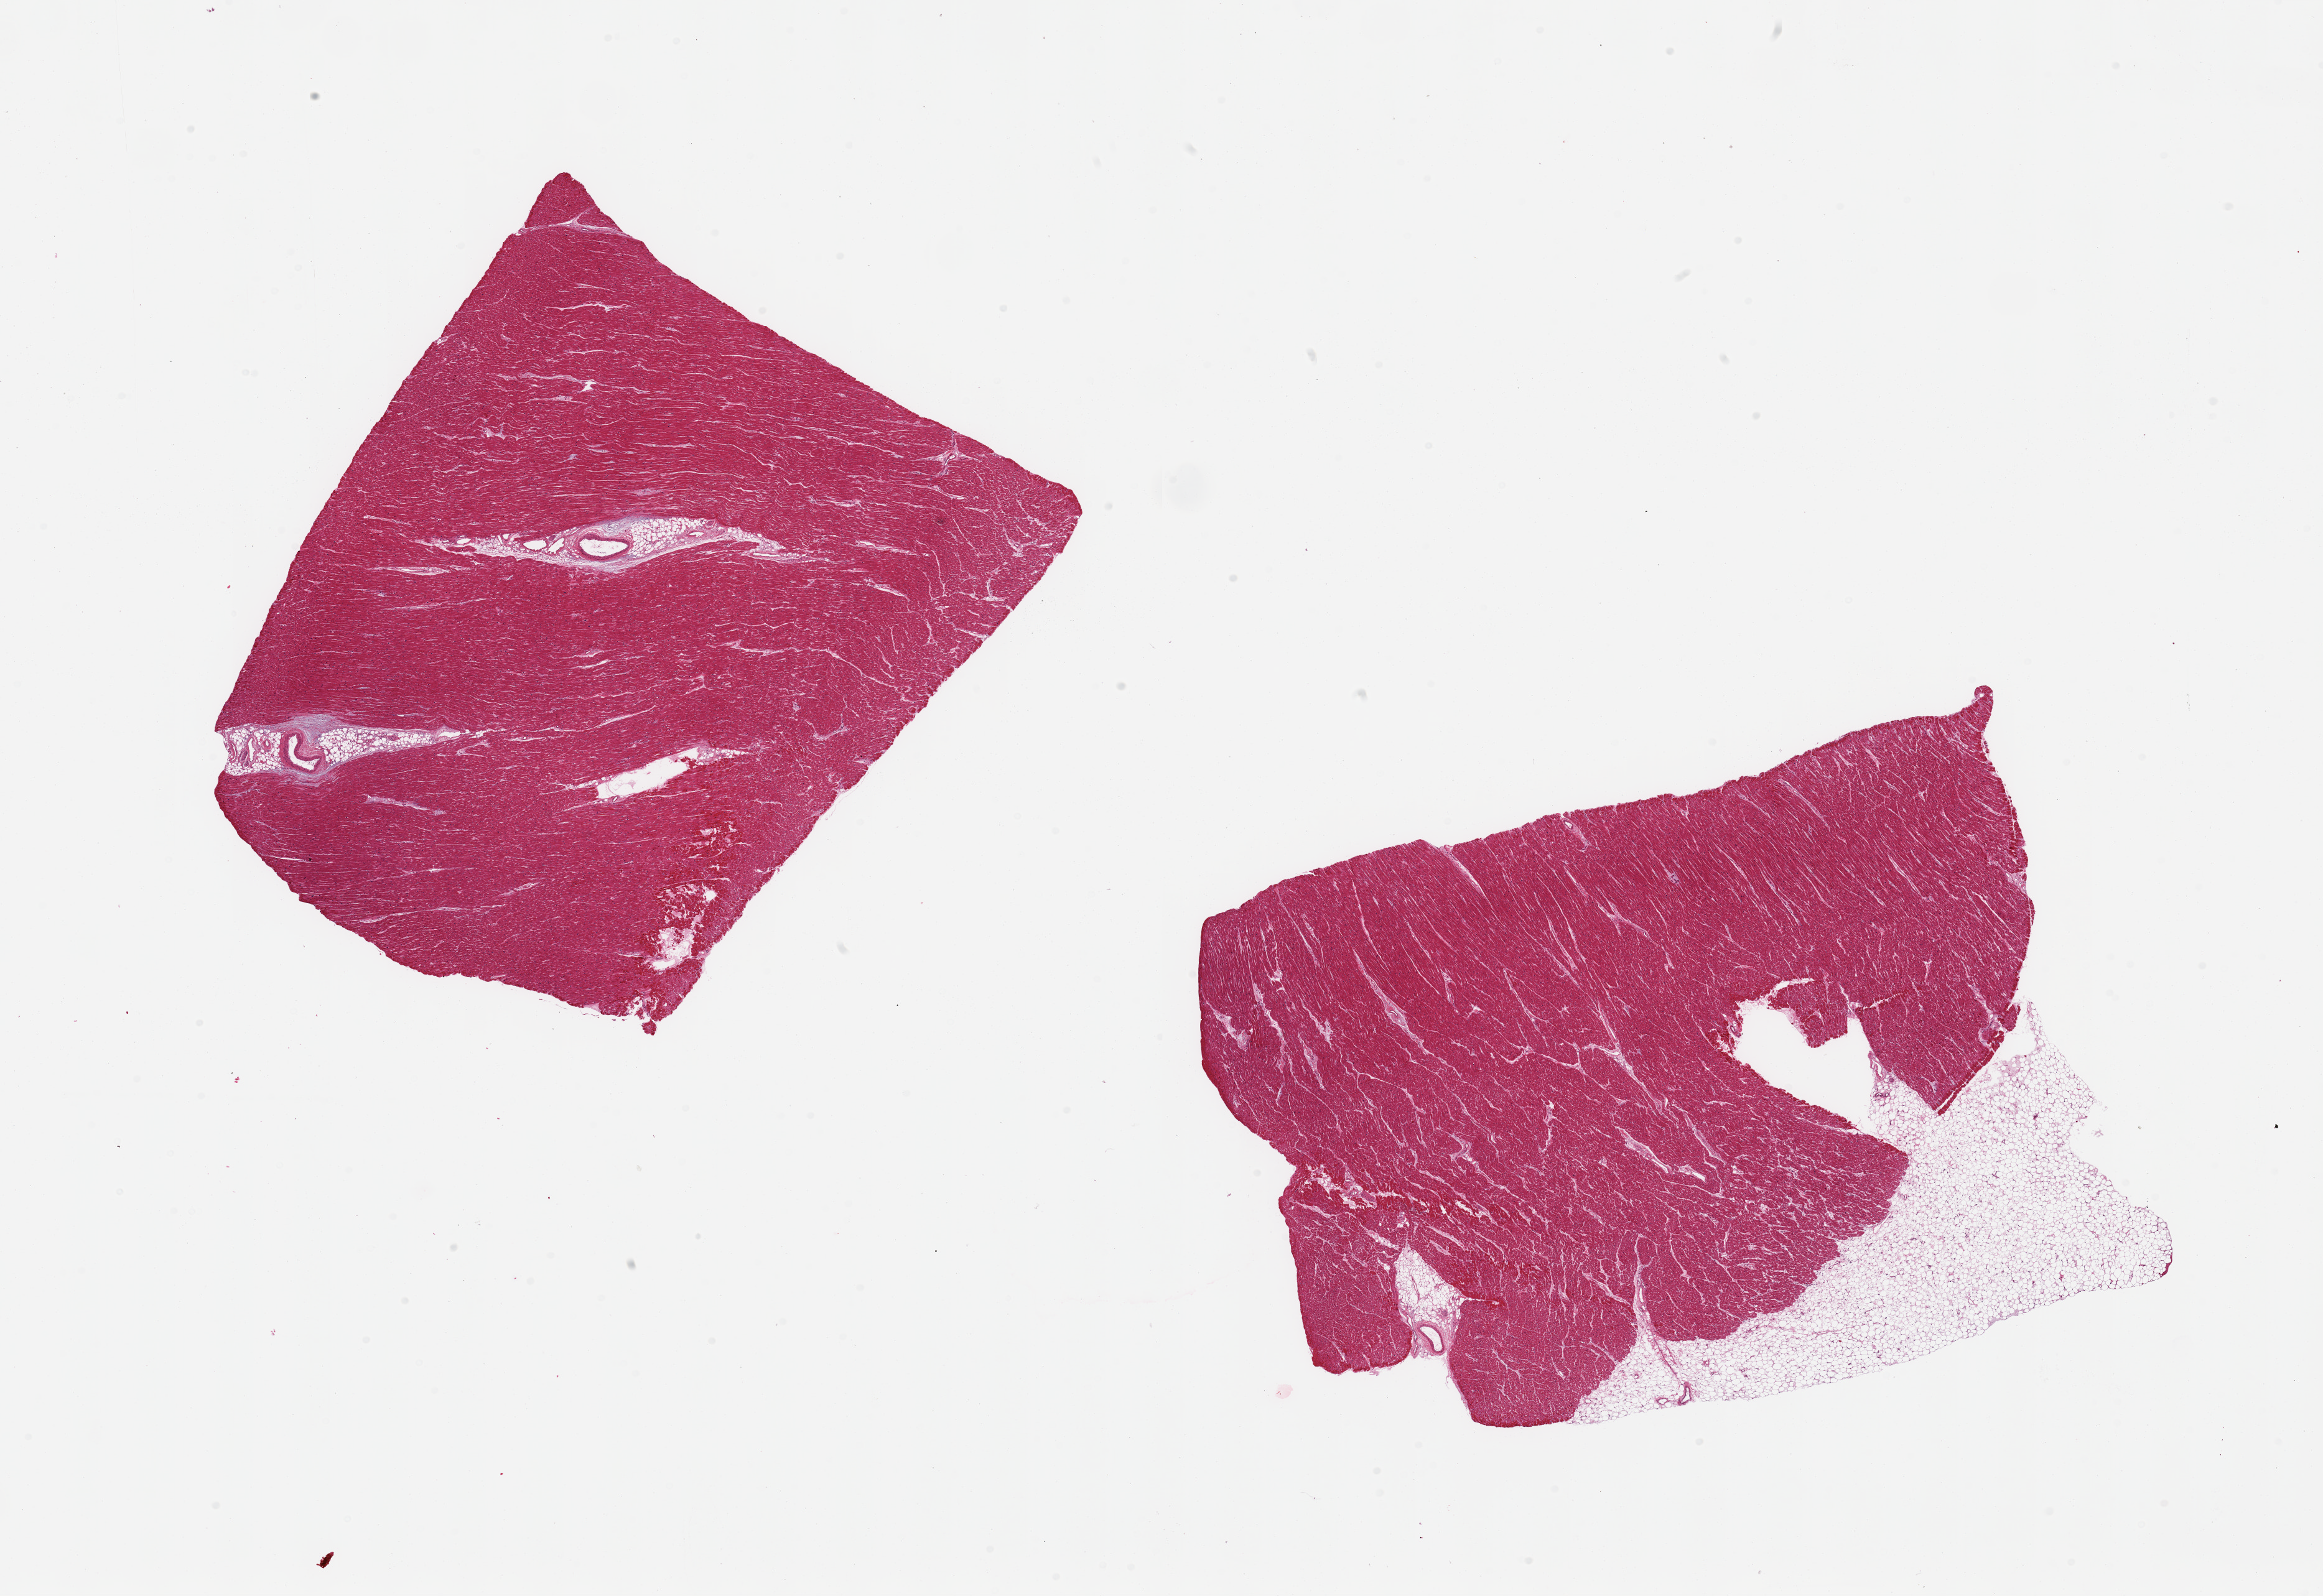
Whole-slide image, H&E stain — a low-resolution overview of the entire scanned area, about 29.5 x 20.3 mm; PAXgene-fixed, paraffin-embedded tissue; sampled site (target tissue): heart; donor tissue sample. Donor: male.
Pathologist's review note for this sample: 2 pieces; fatty streaks along the vessels; one piece with ~25% external fat.